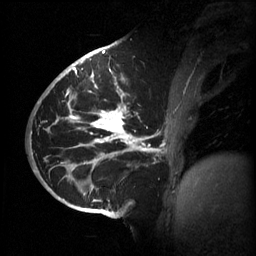
Breast MRI (dynamic contrast-enhanced), one sagittal slice. Position 28 of 60 along the scan axis. 3 images stored at this slice position (order not interpretable as contrast timing). 1.5 T. TE 4.2 ms, TR 11 ms. 2 mm slice thickness. 256 × 256 image matrix, field of view 220 × 220 mm. Patient: female, 51 years.
Annotated regions visible in this slice (semi-automatically segmented with operator editing):
- analysis volume of interest (the breast-tissue region the enhancement analysis was run in; not a lesion): bounding box [x1, y1, x2, y2] px = [63, 80, 187, 201]
- tumour enhancement mask (voxels above the 70 % enhancement threshold inside the analysis volume of interest): [66, 80, 164, 201]